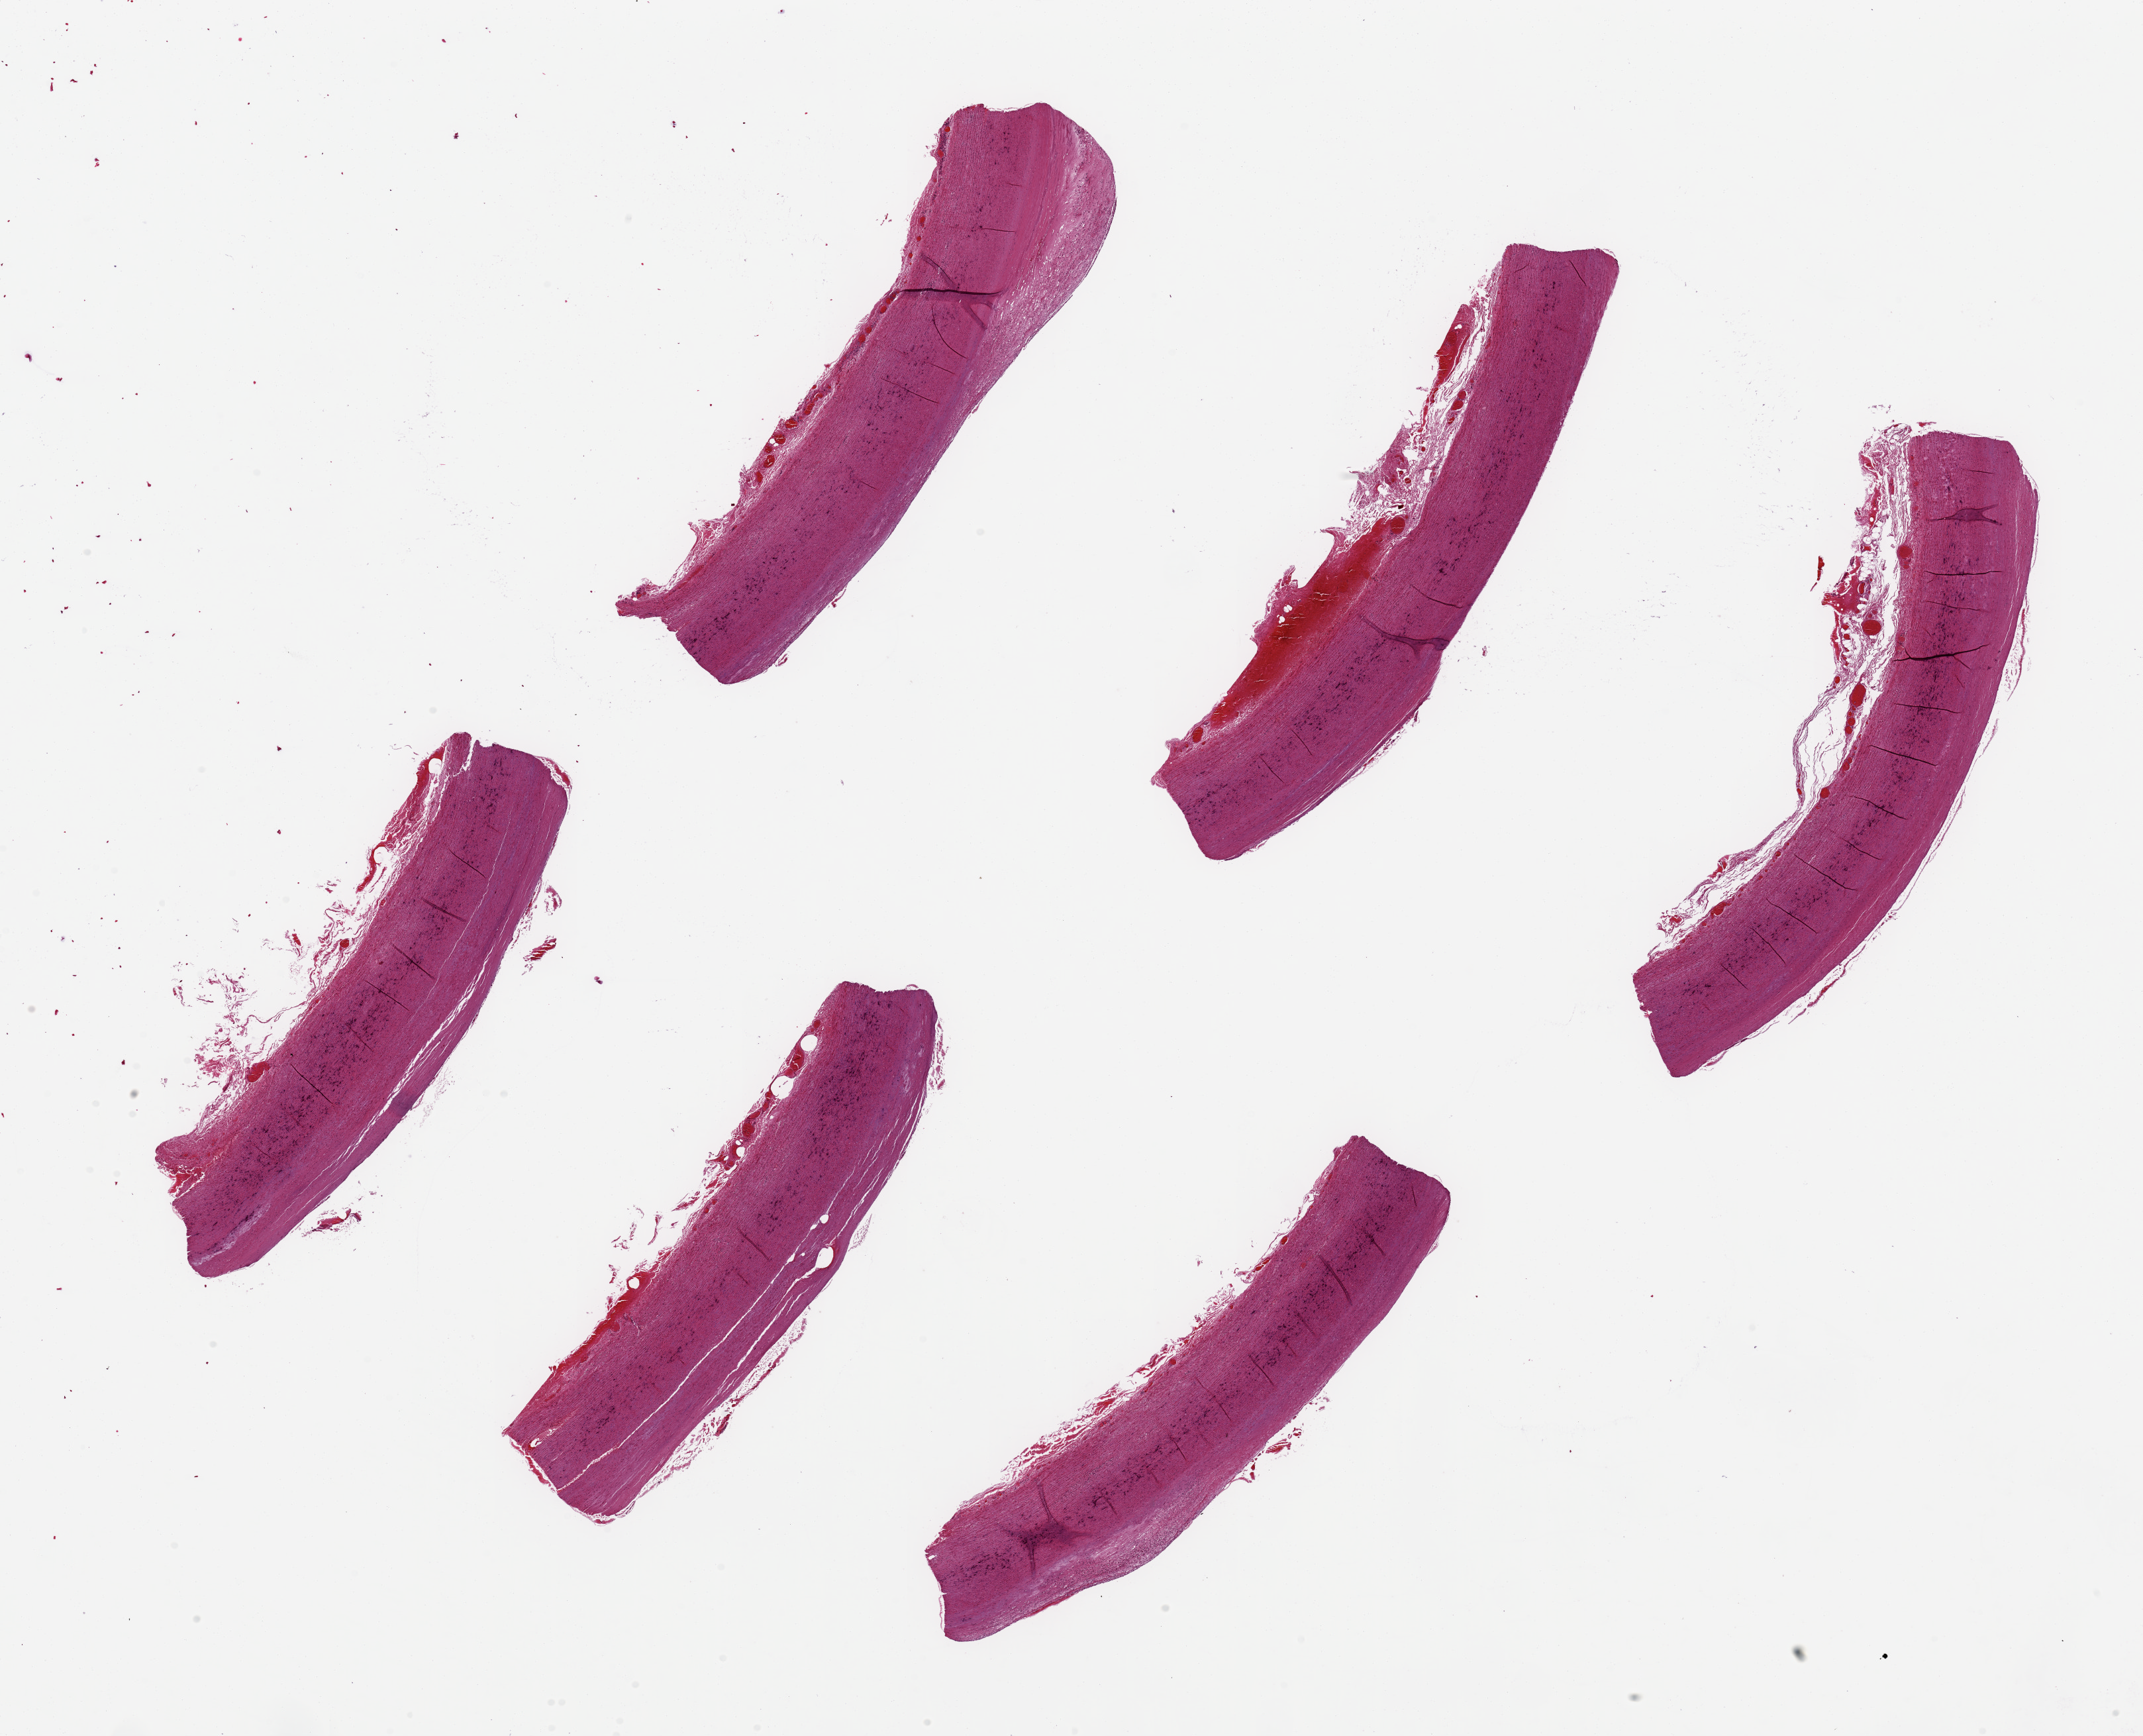
Whole-slide image, H&E stain — shown as a low-resolution overview of the whole scanned area (about 25.6 x 20.7 mm, from a 20x scan); PAXgene-fixed paraffin-embedded (PFPE) section; sampled site (target tissue): aorta; donor tissue sample.
Review note (as recorded): 6 pieces ~8x1.5mm, several with up to 0.4mm atheromatous plaque.